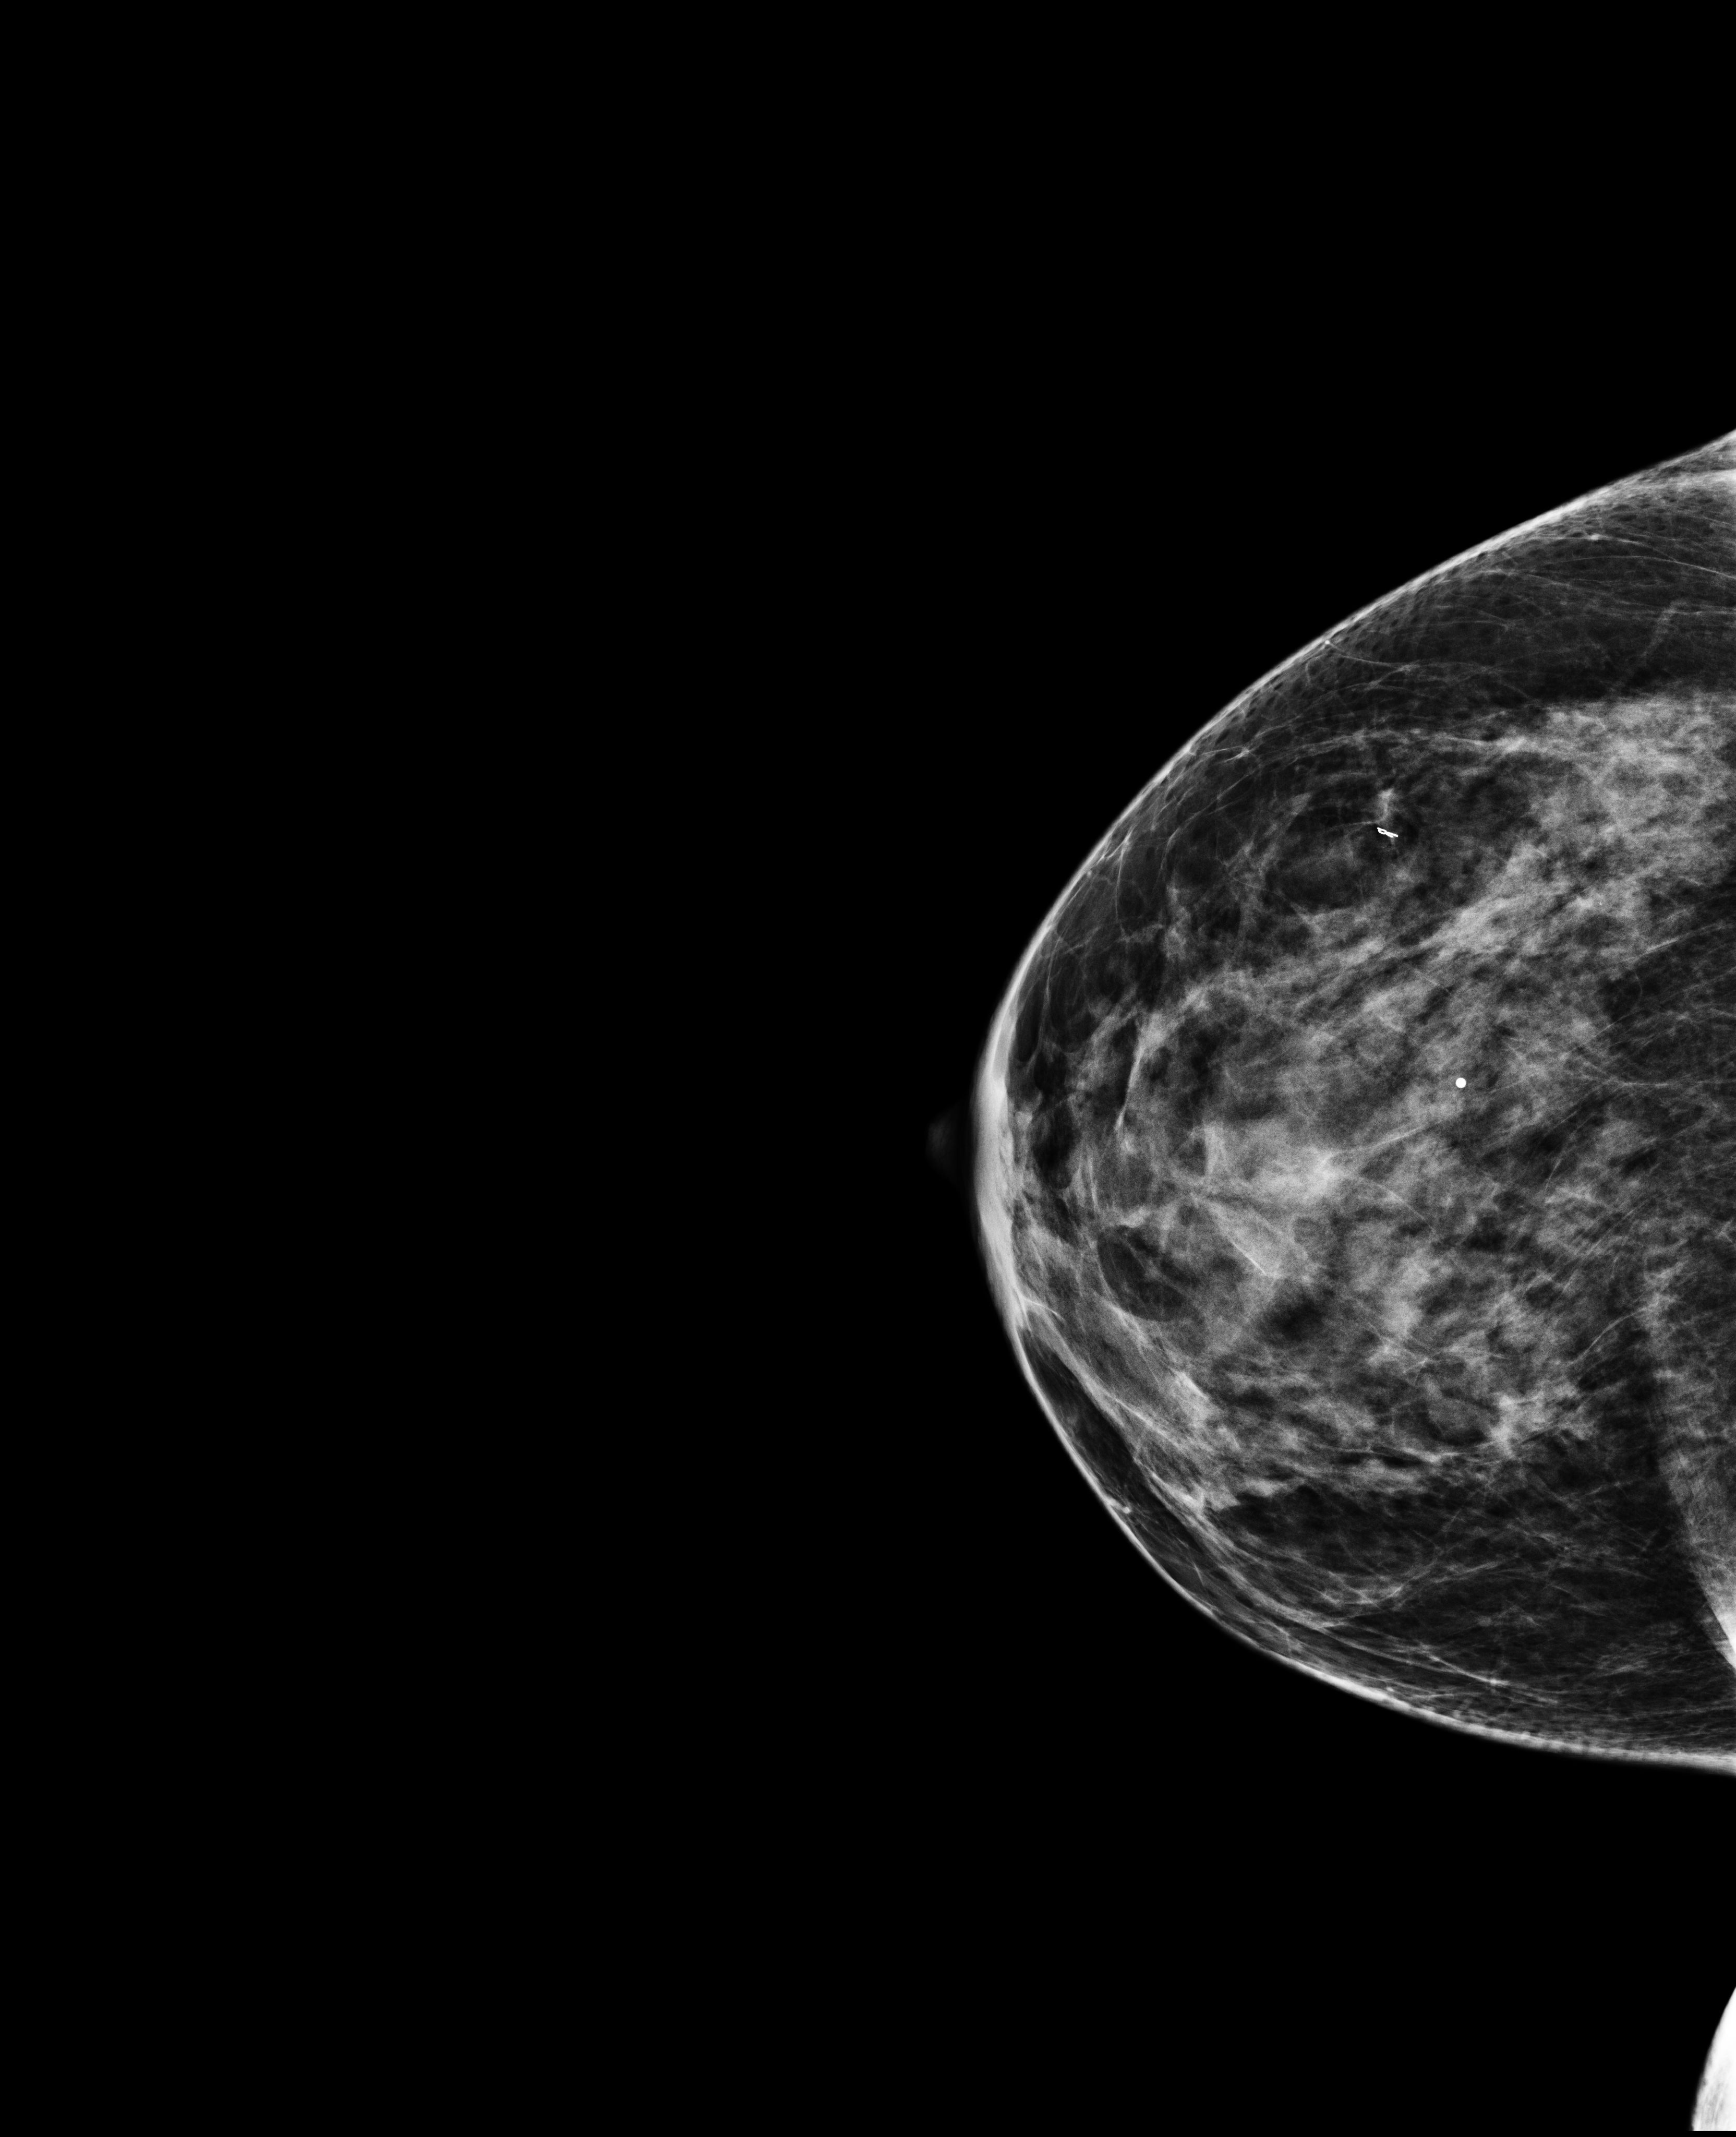
Screening examination; system: Selenia Dimensions.
Image type: full-field digital mammogram. Breast: right. Projection: cranio-caudal projection.